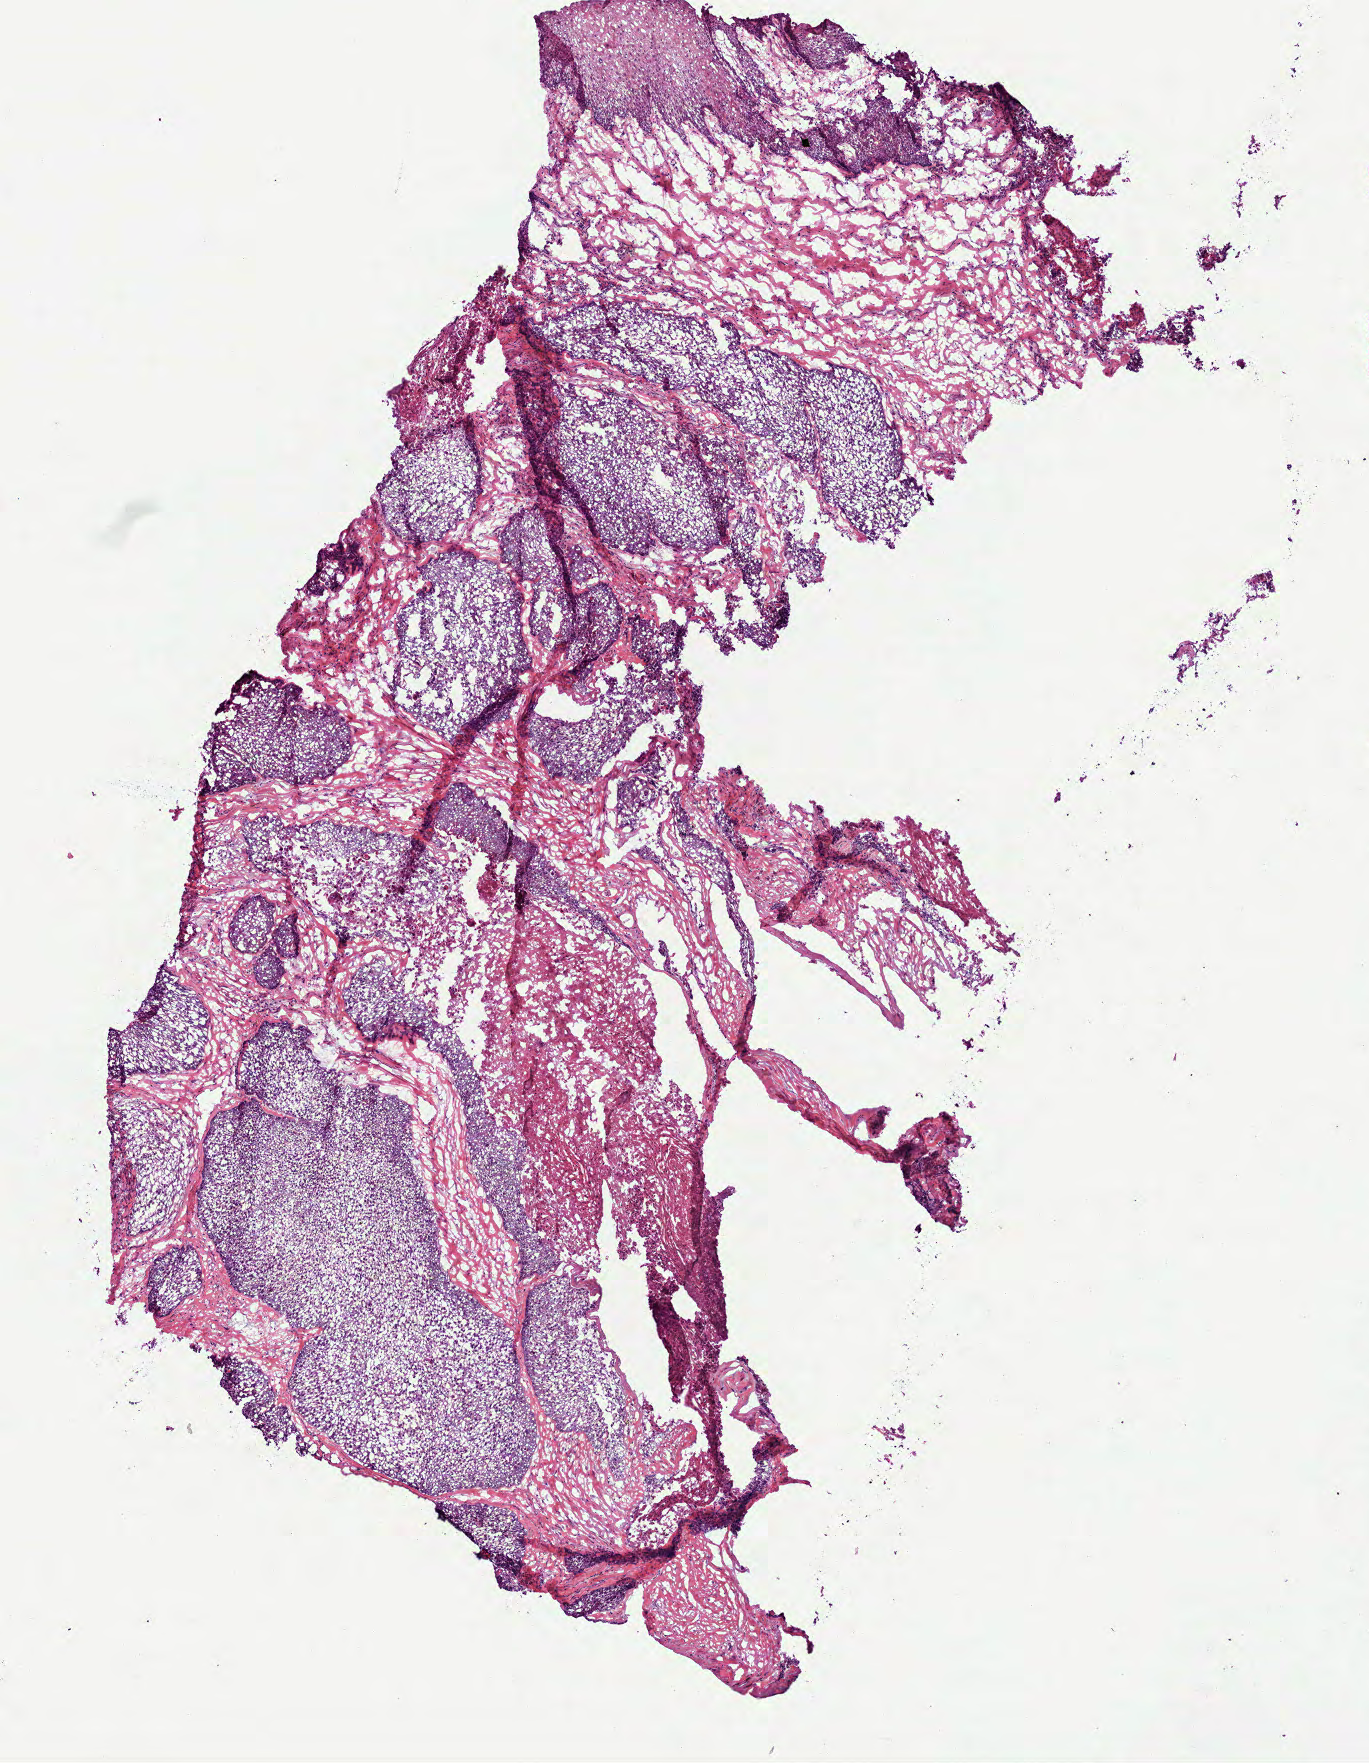
H&E-stained whole-slide image — shown as a low-resolution overview of the whole scanned area (about 5.5 x 7.1 mm, from a 40x scan), frozen section from the top of the tissue portion, sample: primary tumour, head and neck. Male, age 65 years at initial diagnosis. Histologic grade: G2 (moderately differentiated). Slide review estimates, as recorded: tumour cells 58%, tumour nuclei 85%, normal cells 5%, stromal cells 35%, necrosis 2%.
Diagnosis: Squamous cell carcinoma, NOS (overlapping lesion of lip, oral cavity and pharynx). AJCC pathologic stage: III (6th edition). Lymph nodes positive (case pathology): 0 of 25 examined.